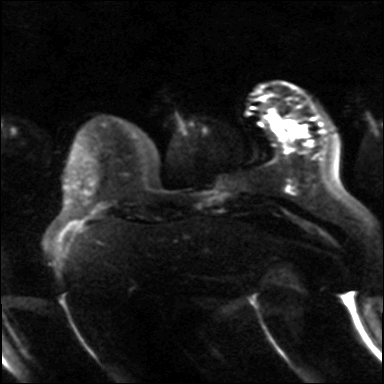
Breast MRI, one axial slice. Slice 7 of 36 in the series (ordered by position). Diffusion-weighted series; image 2 of 4 stored at this slice position (different b-values; order by instance number). 3 T. 4 mm slice thickness. 384 × 384 image matrix, field of view 320 × 320 mm. Female patient.
Annotated regions visible in this slice (expert manual segmentation):
- tumour on diffusion-weighted imaging: bounding box [x1, y1, x2, y2] px = [299, 128, 303, 132]